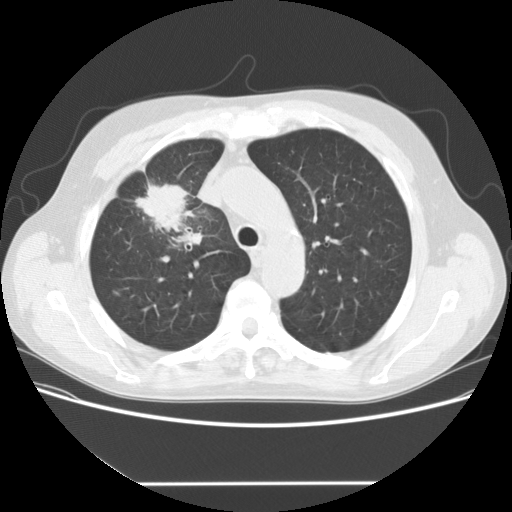
Axial slice from a low-dose chest CT screening exam. Baseline screening round. Lung window (W 1500 / L -600 HU). Standard (soft-tissue) reconstruction kernel (STANDARD). 512 × 512 image matrix, field of view 360 × 360 mm. Male participant, aged 56 years at enrolment.
• Lesion marked by an expert reader, bounding box (x1, y1, x2, y2) in pixels: (127, 171, 214, 247).
• The screening reader recorded 2 non-calcified nodules or masses ≥4 mm on this exam; which of them this box marks is not recorded.
• Official screen result: positive, change unspecified: nodule(s) >= 4 mm or enlarging nodule(s), mass(es), or other non-specific abnormalities suspicious for lung cancer.
• Later outcome: lung cancer diagnosed 120 days after this screen — adenocarcinoma, NOS, right upper lobe, stage IIIA (AJCC 6th edition), 34 mm at pathology.